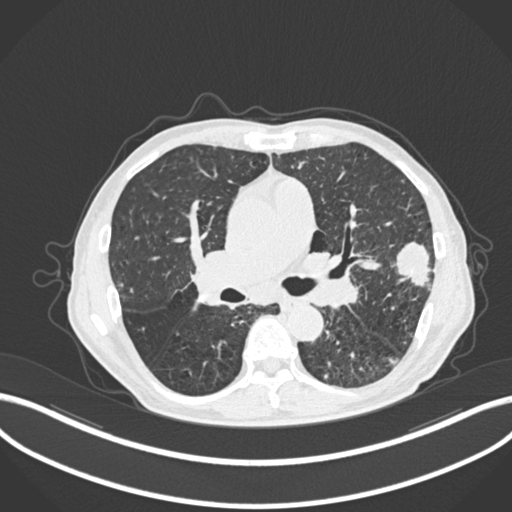
Chest CT, one axial slice; position 137 of 287 along the scan axis; reconstruction kernel B30f; lung window (W 1500 / L -600 HU); 1 mm slice thickness; 512 × 512 image matrix. Male patient, age 74 years. Case-level facts recorded for this patient, not image findings: clinical TNM (as recorded): T2a N1 M0.
Annotated regions visible in this slice (rectangle marked by the reading radiologist):
- lung tumour (recorded histology: adenocarcinoma): bounding box <392,240,432,292> (left, top, right, bottom; pixels)